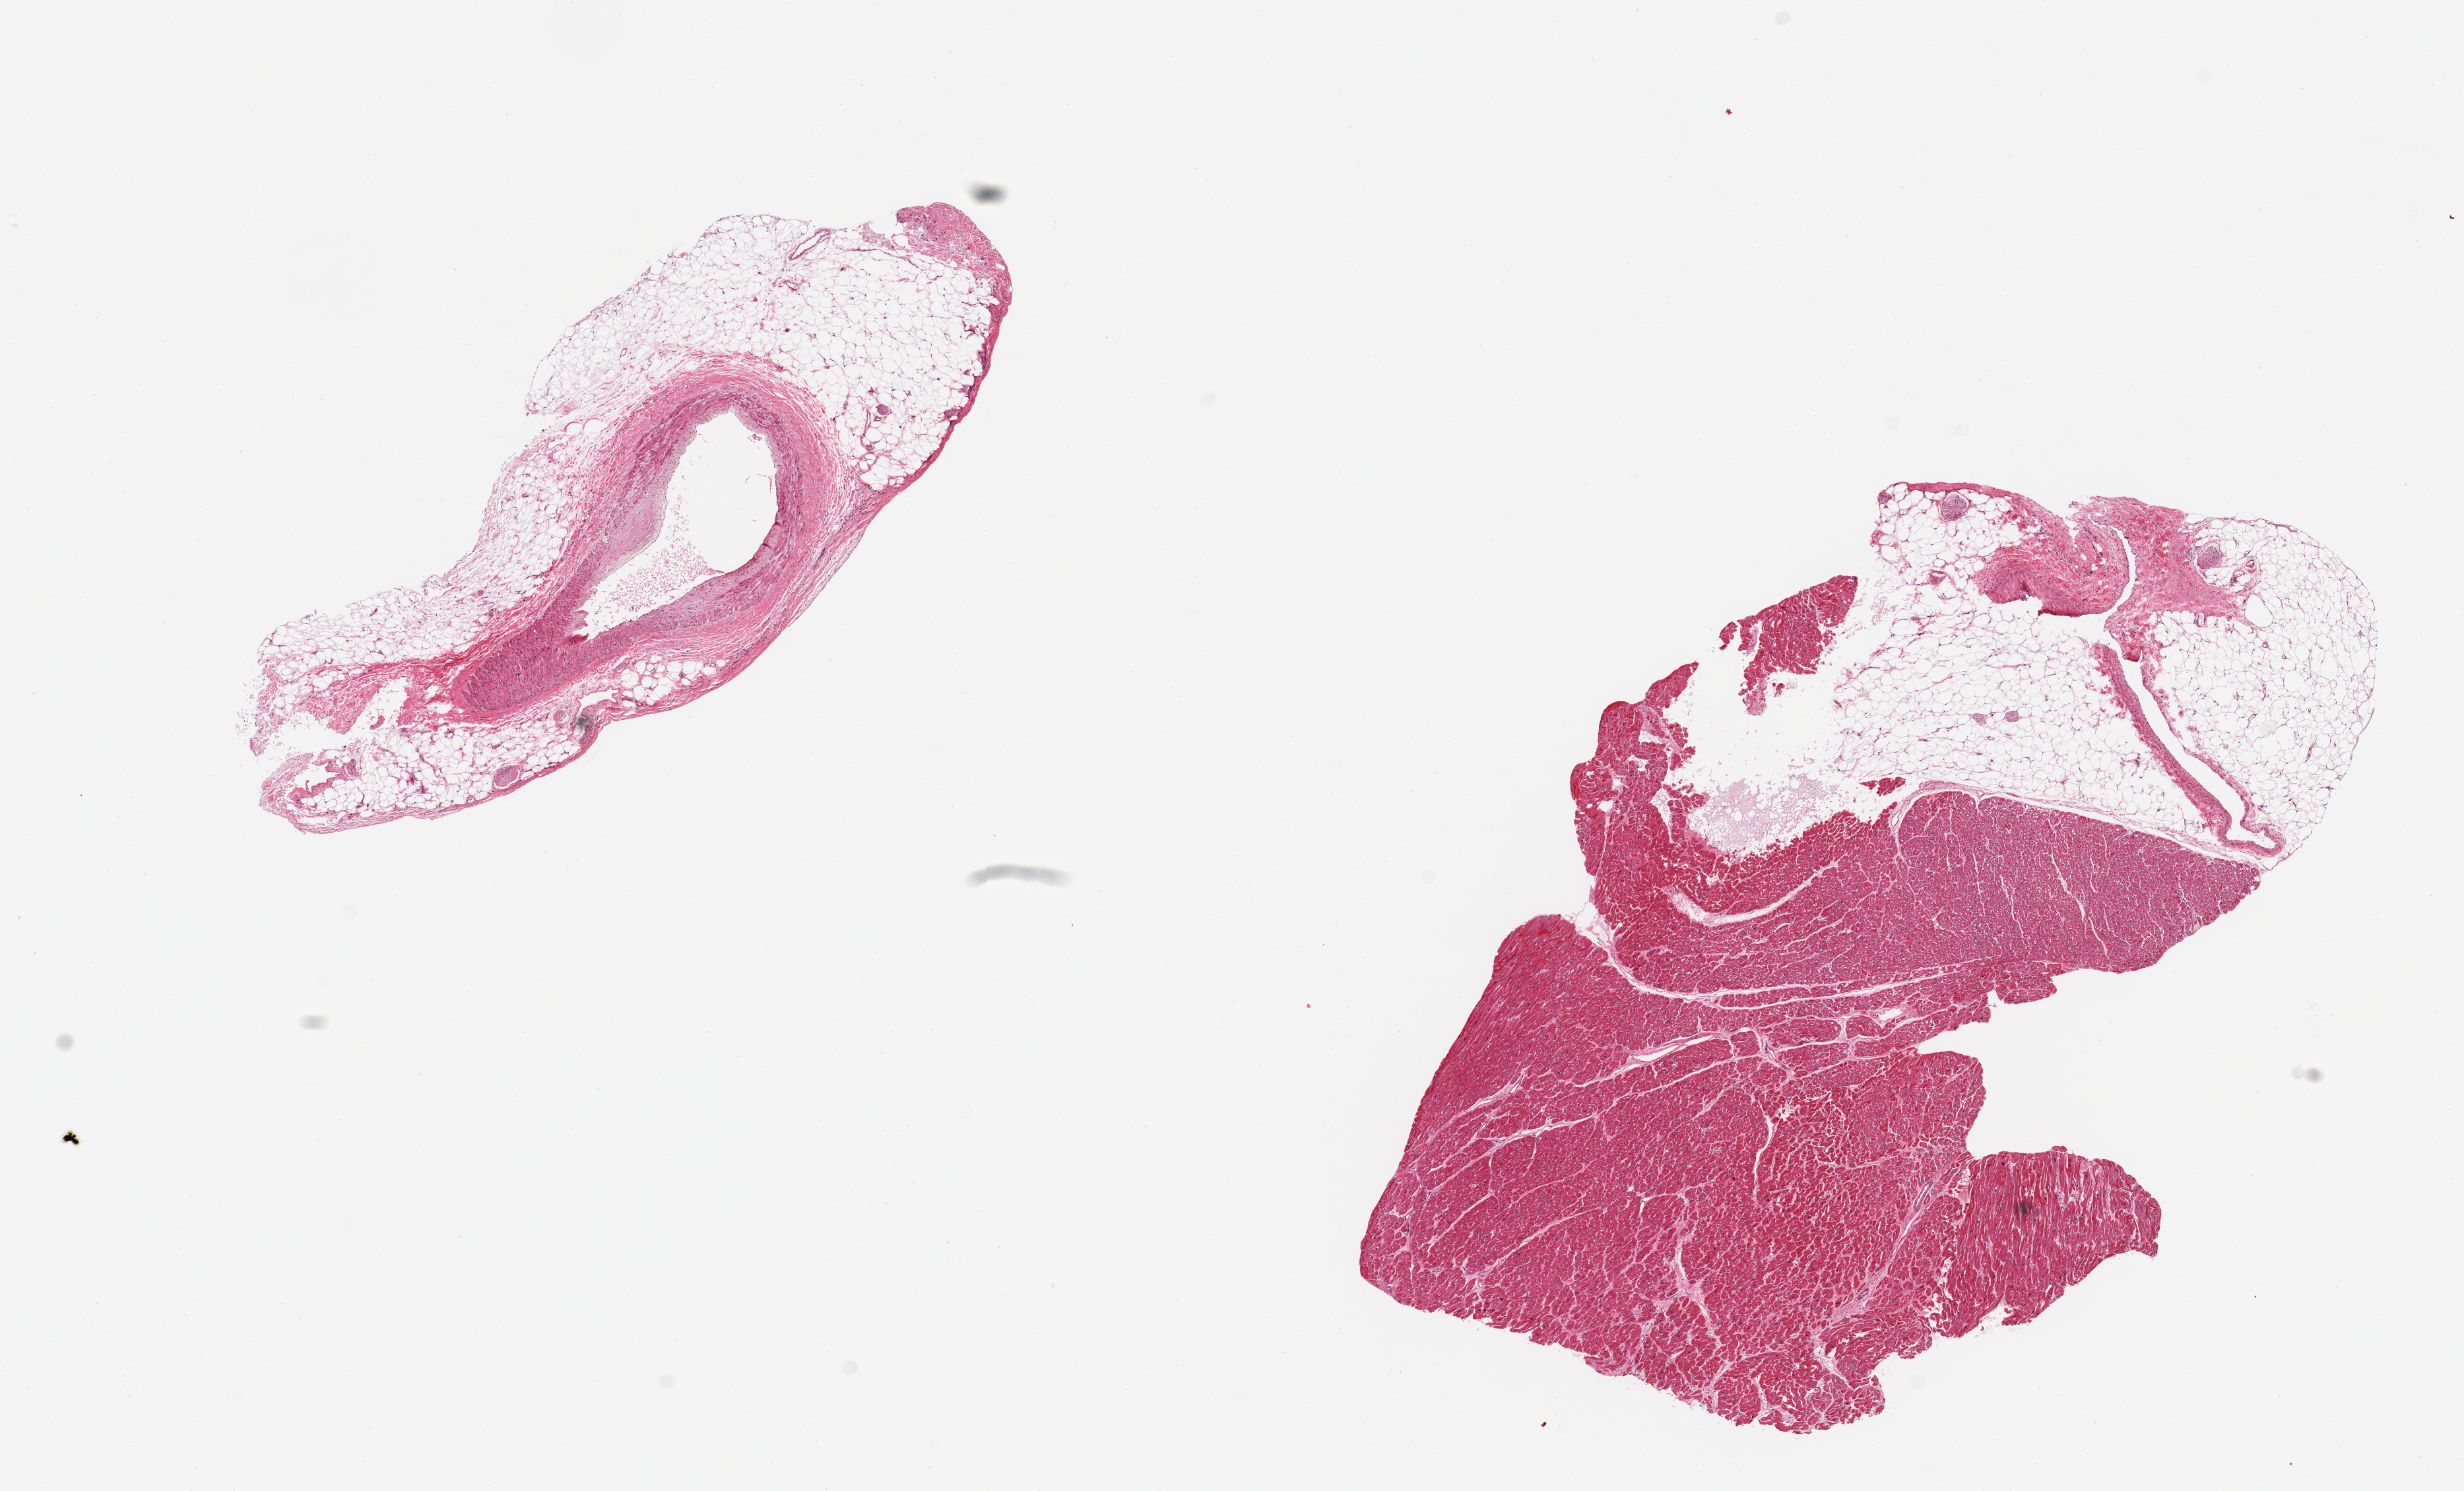
Digitized hematoxylin and eosin (H&E)-stained section, low-resolution overview of the scanned area, about 14.8 x 8.9 mm. Donor: female.
* specimen: PAXgene-fixed paraffin-embedded (PFPE) section; section of coronary artery (target tissue); donor tissue sample